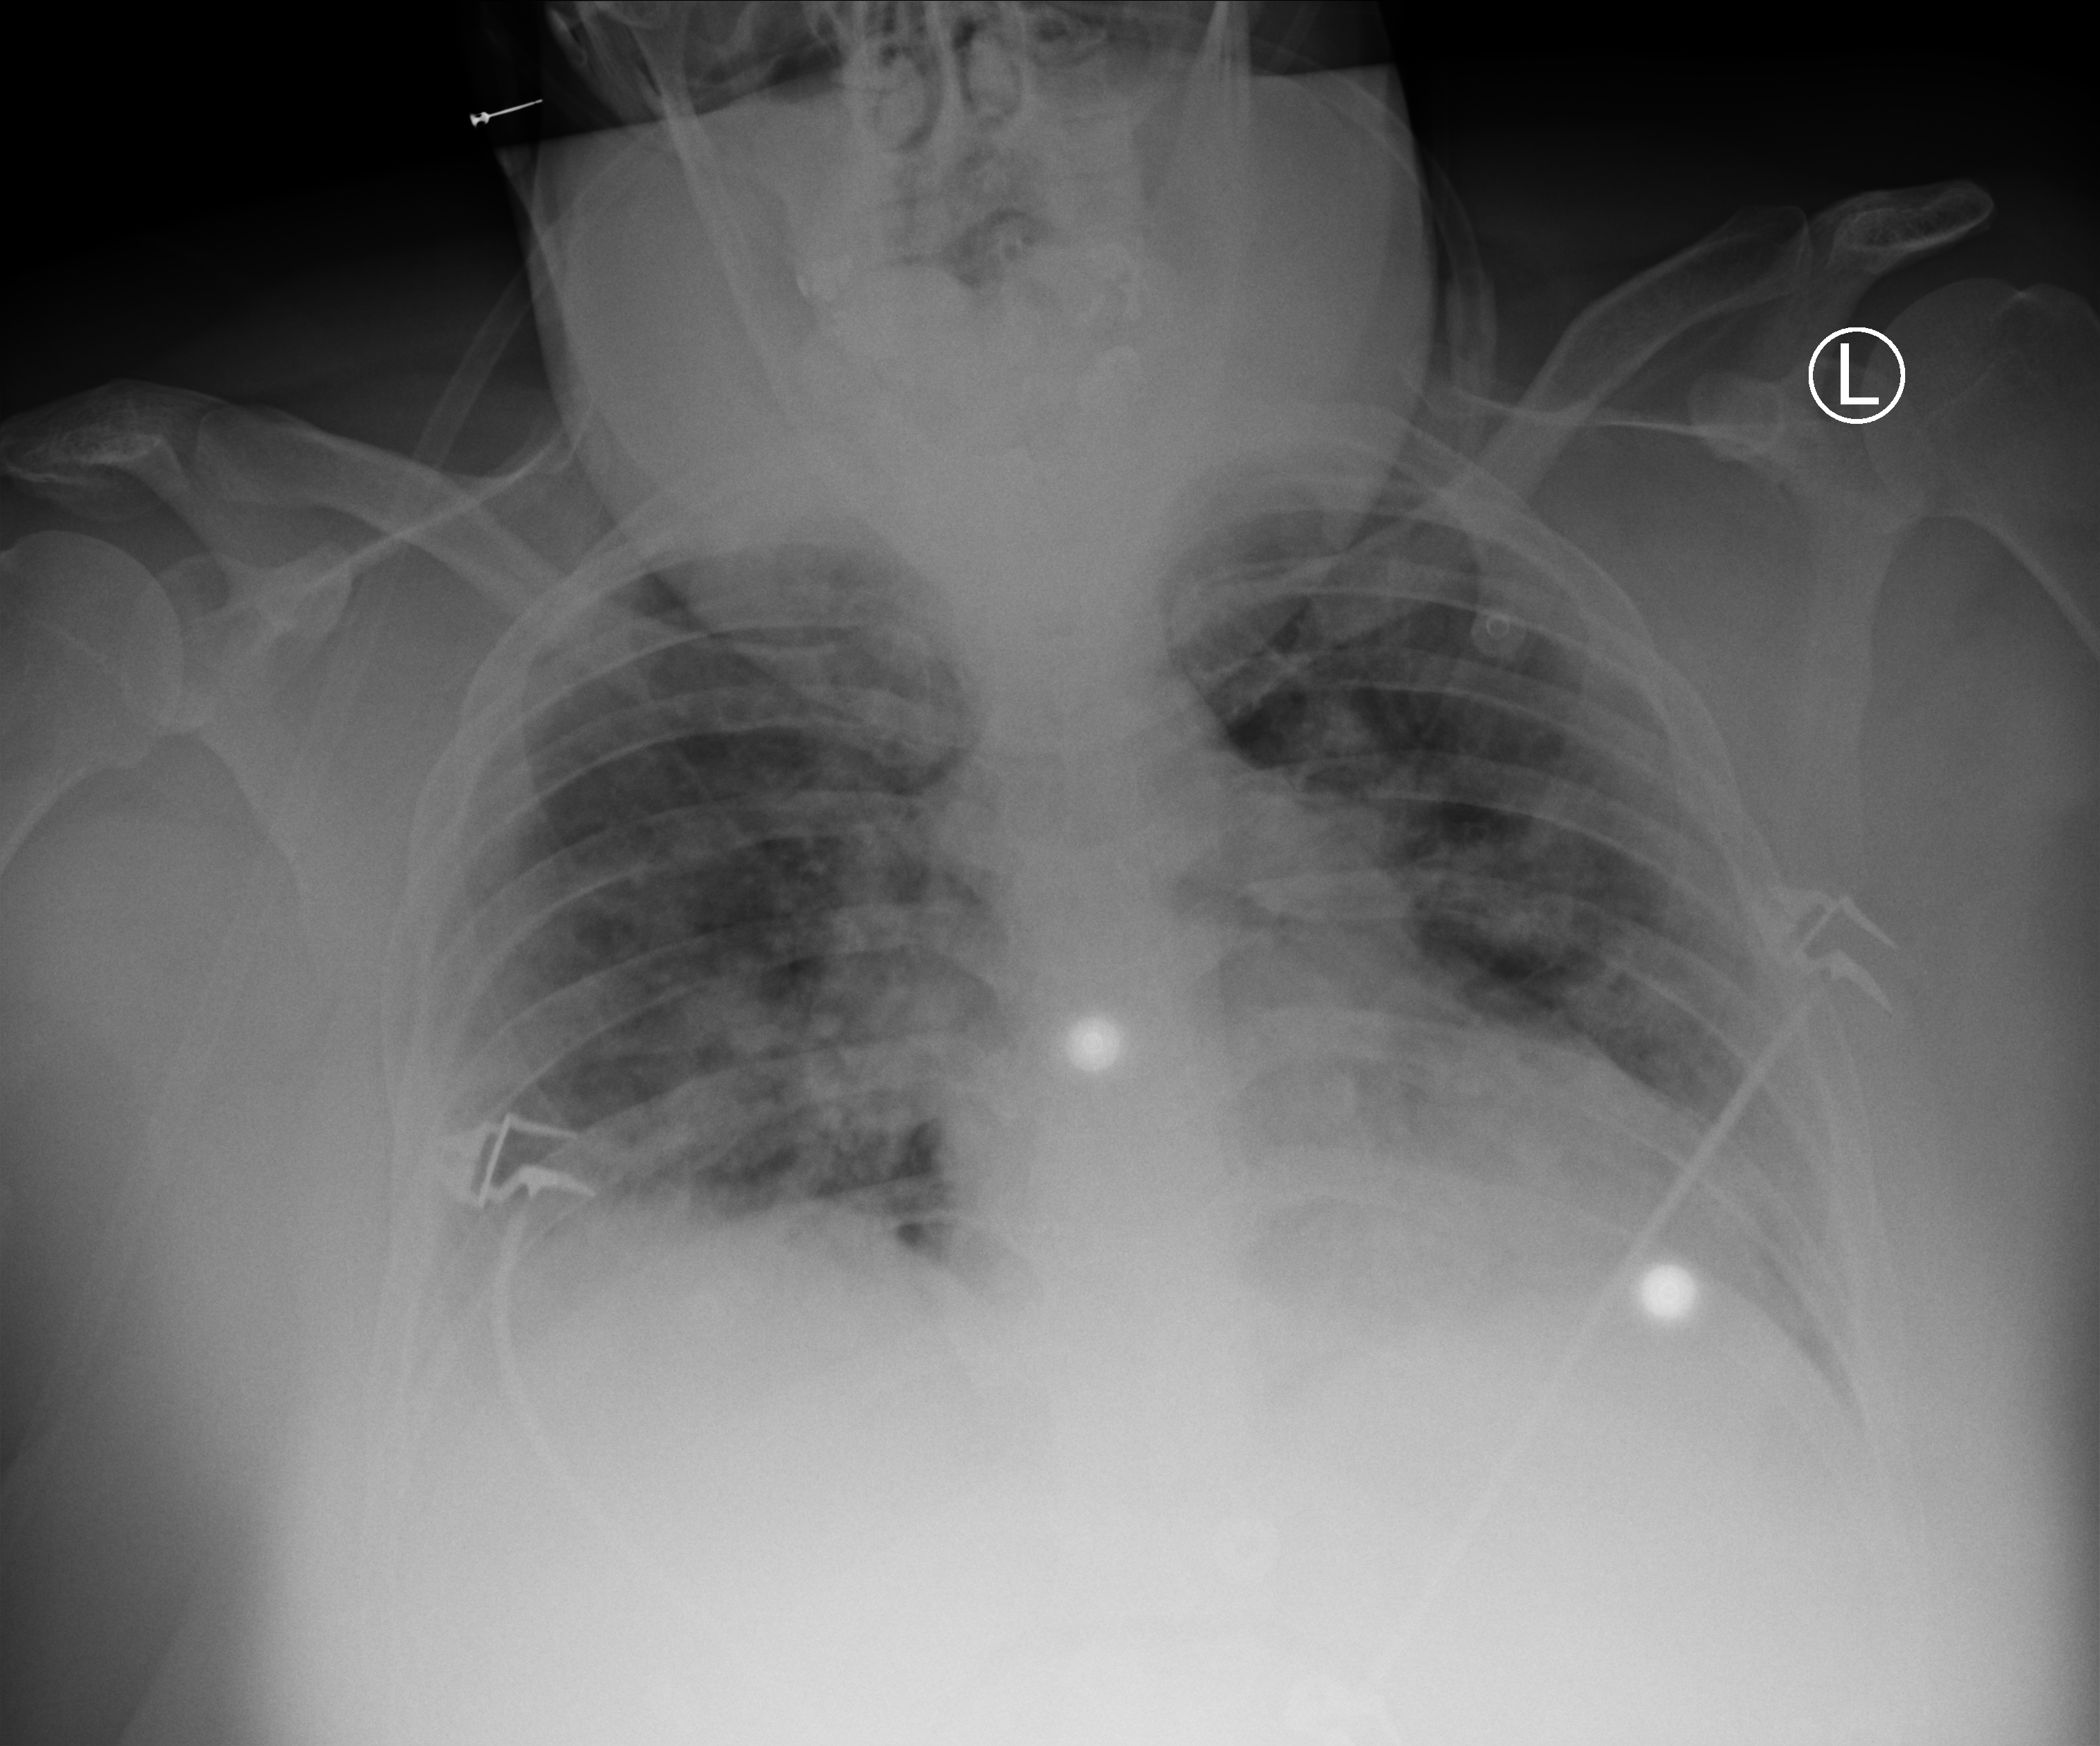
Portable chest radiograph; anteroposterior (AP) projection. Female patient hospitalised with COVID-19, age 18–59 years.
From the hospital-stay record, not from the radiograph (when in the stay this image was taken is not recorded): mechanically ventilated during this hospital stay: no.